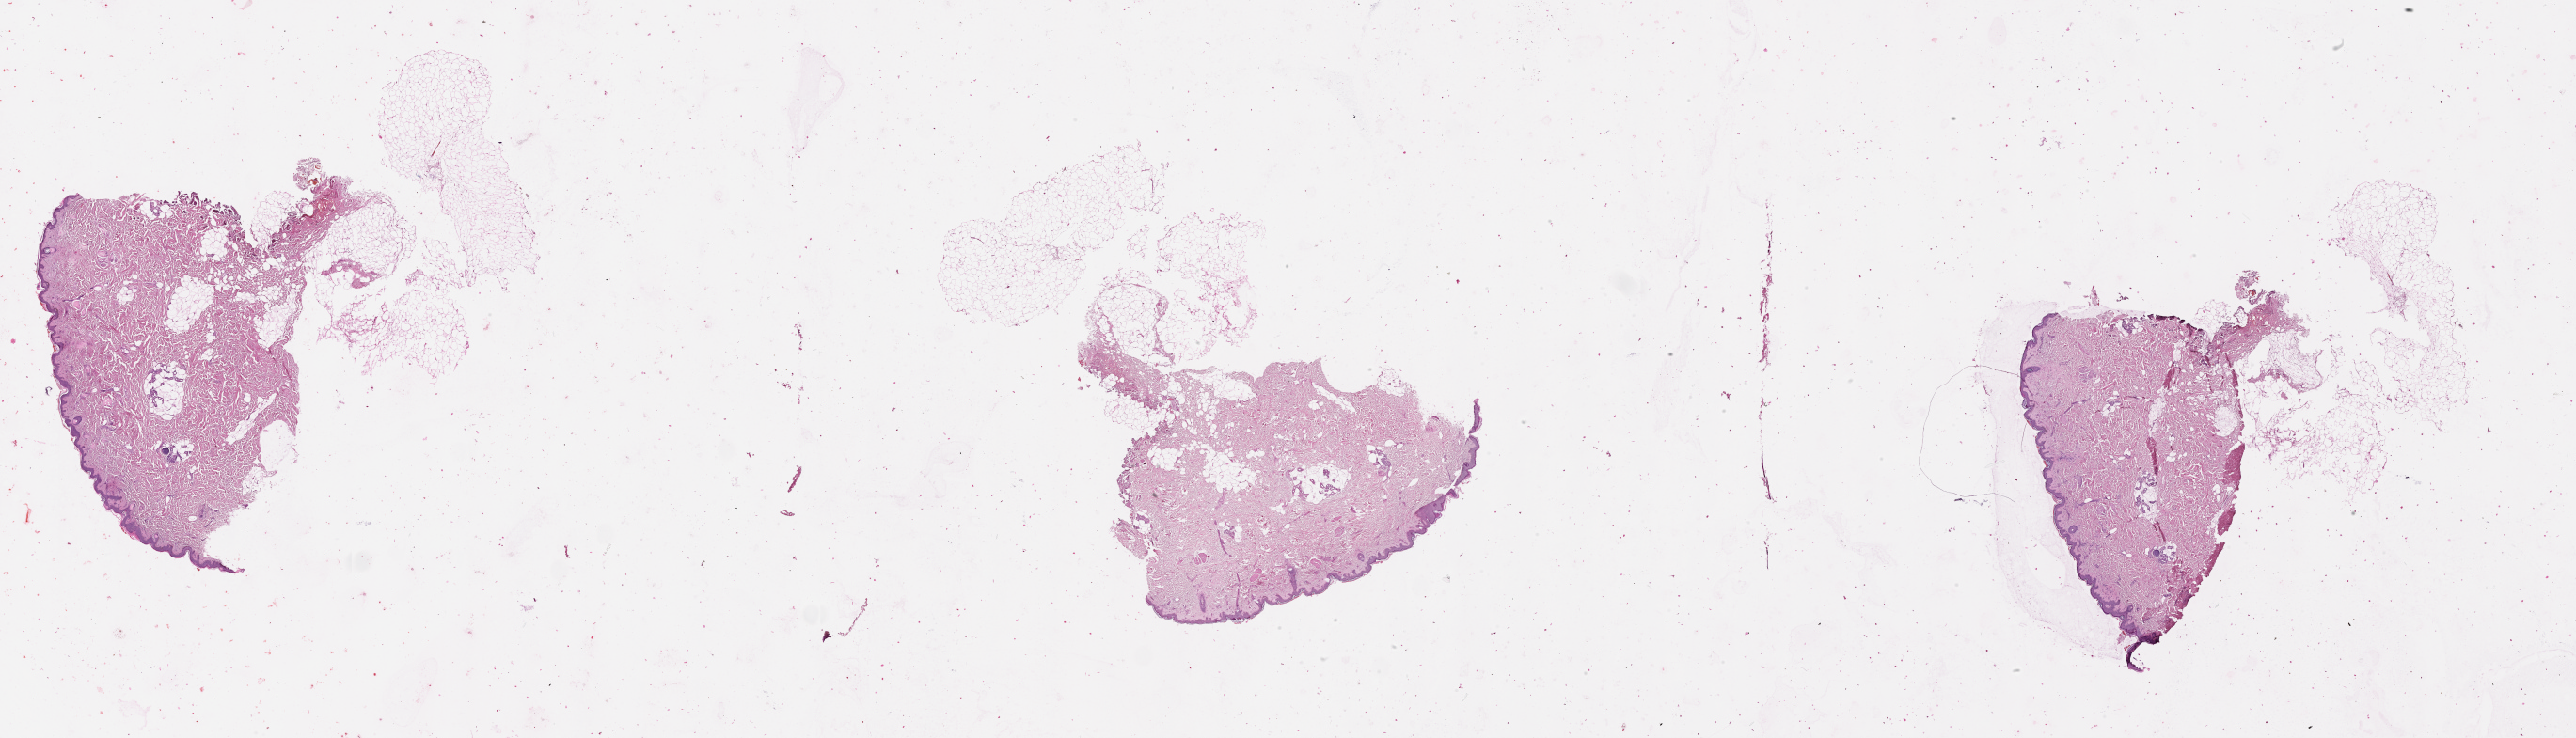
Hematoxylin and eosin (H&E) stained whole-slide image, whole scanned area (about 44.1 x 12.6 mm) shown as a low-resolution overview; normal (non-tumour) tissue sample, sampled site: shoulder. Female, 55 y/o.
• this section: normal (non-tumour) tissue from the same patient
• patient diagnosis: Malignant melanoma, NOS